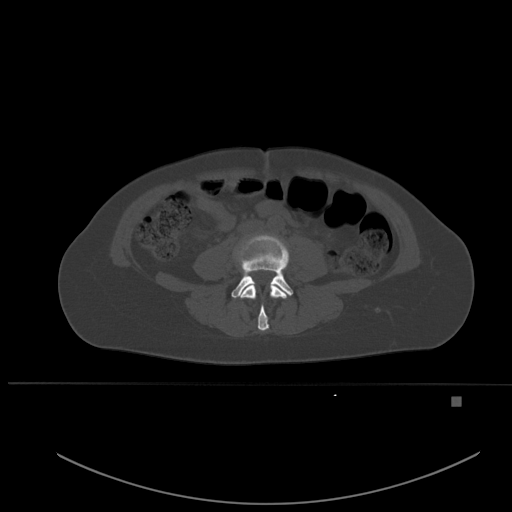
CT including the spine, one axial slice; position 181 of 651 along the scan axis; bone window (W 1800 / L 400 HU); 512 × 512 image matrix, field of view 443 × 443 mm. Female patient, age 49 years. Case-level facts recorded for this patient, not image findings: primary cancer: breast.
Structures marked on this image (semi-automatic segmentation, software-assisted and operator-edited):
- L3 vertebra: bounding box (x1, y1, x2, y2) in pixels: (240, 284, 287, 331)
- L4 vertebra: (231, 235, 293, 298)